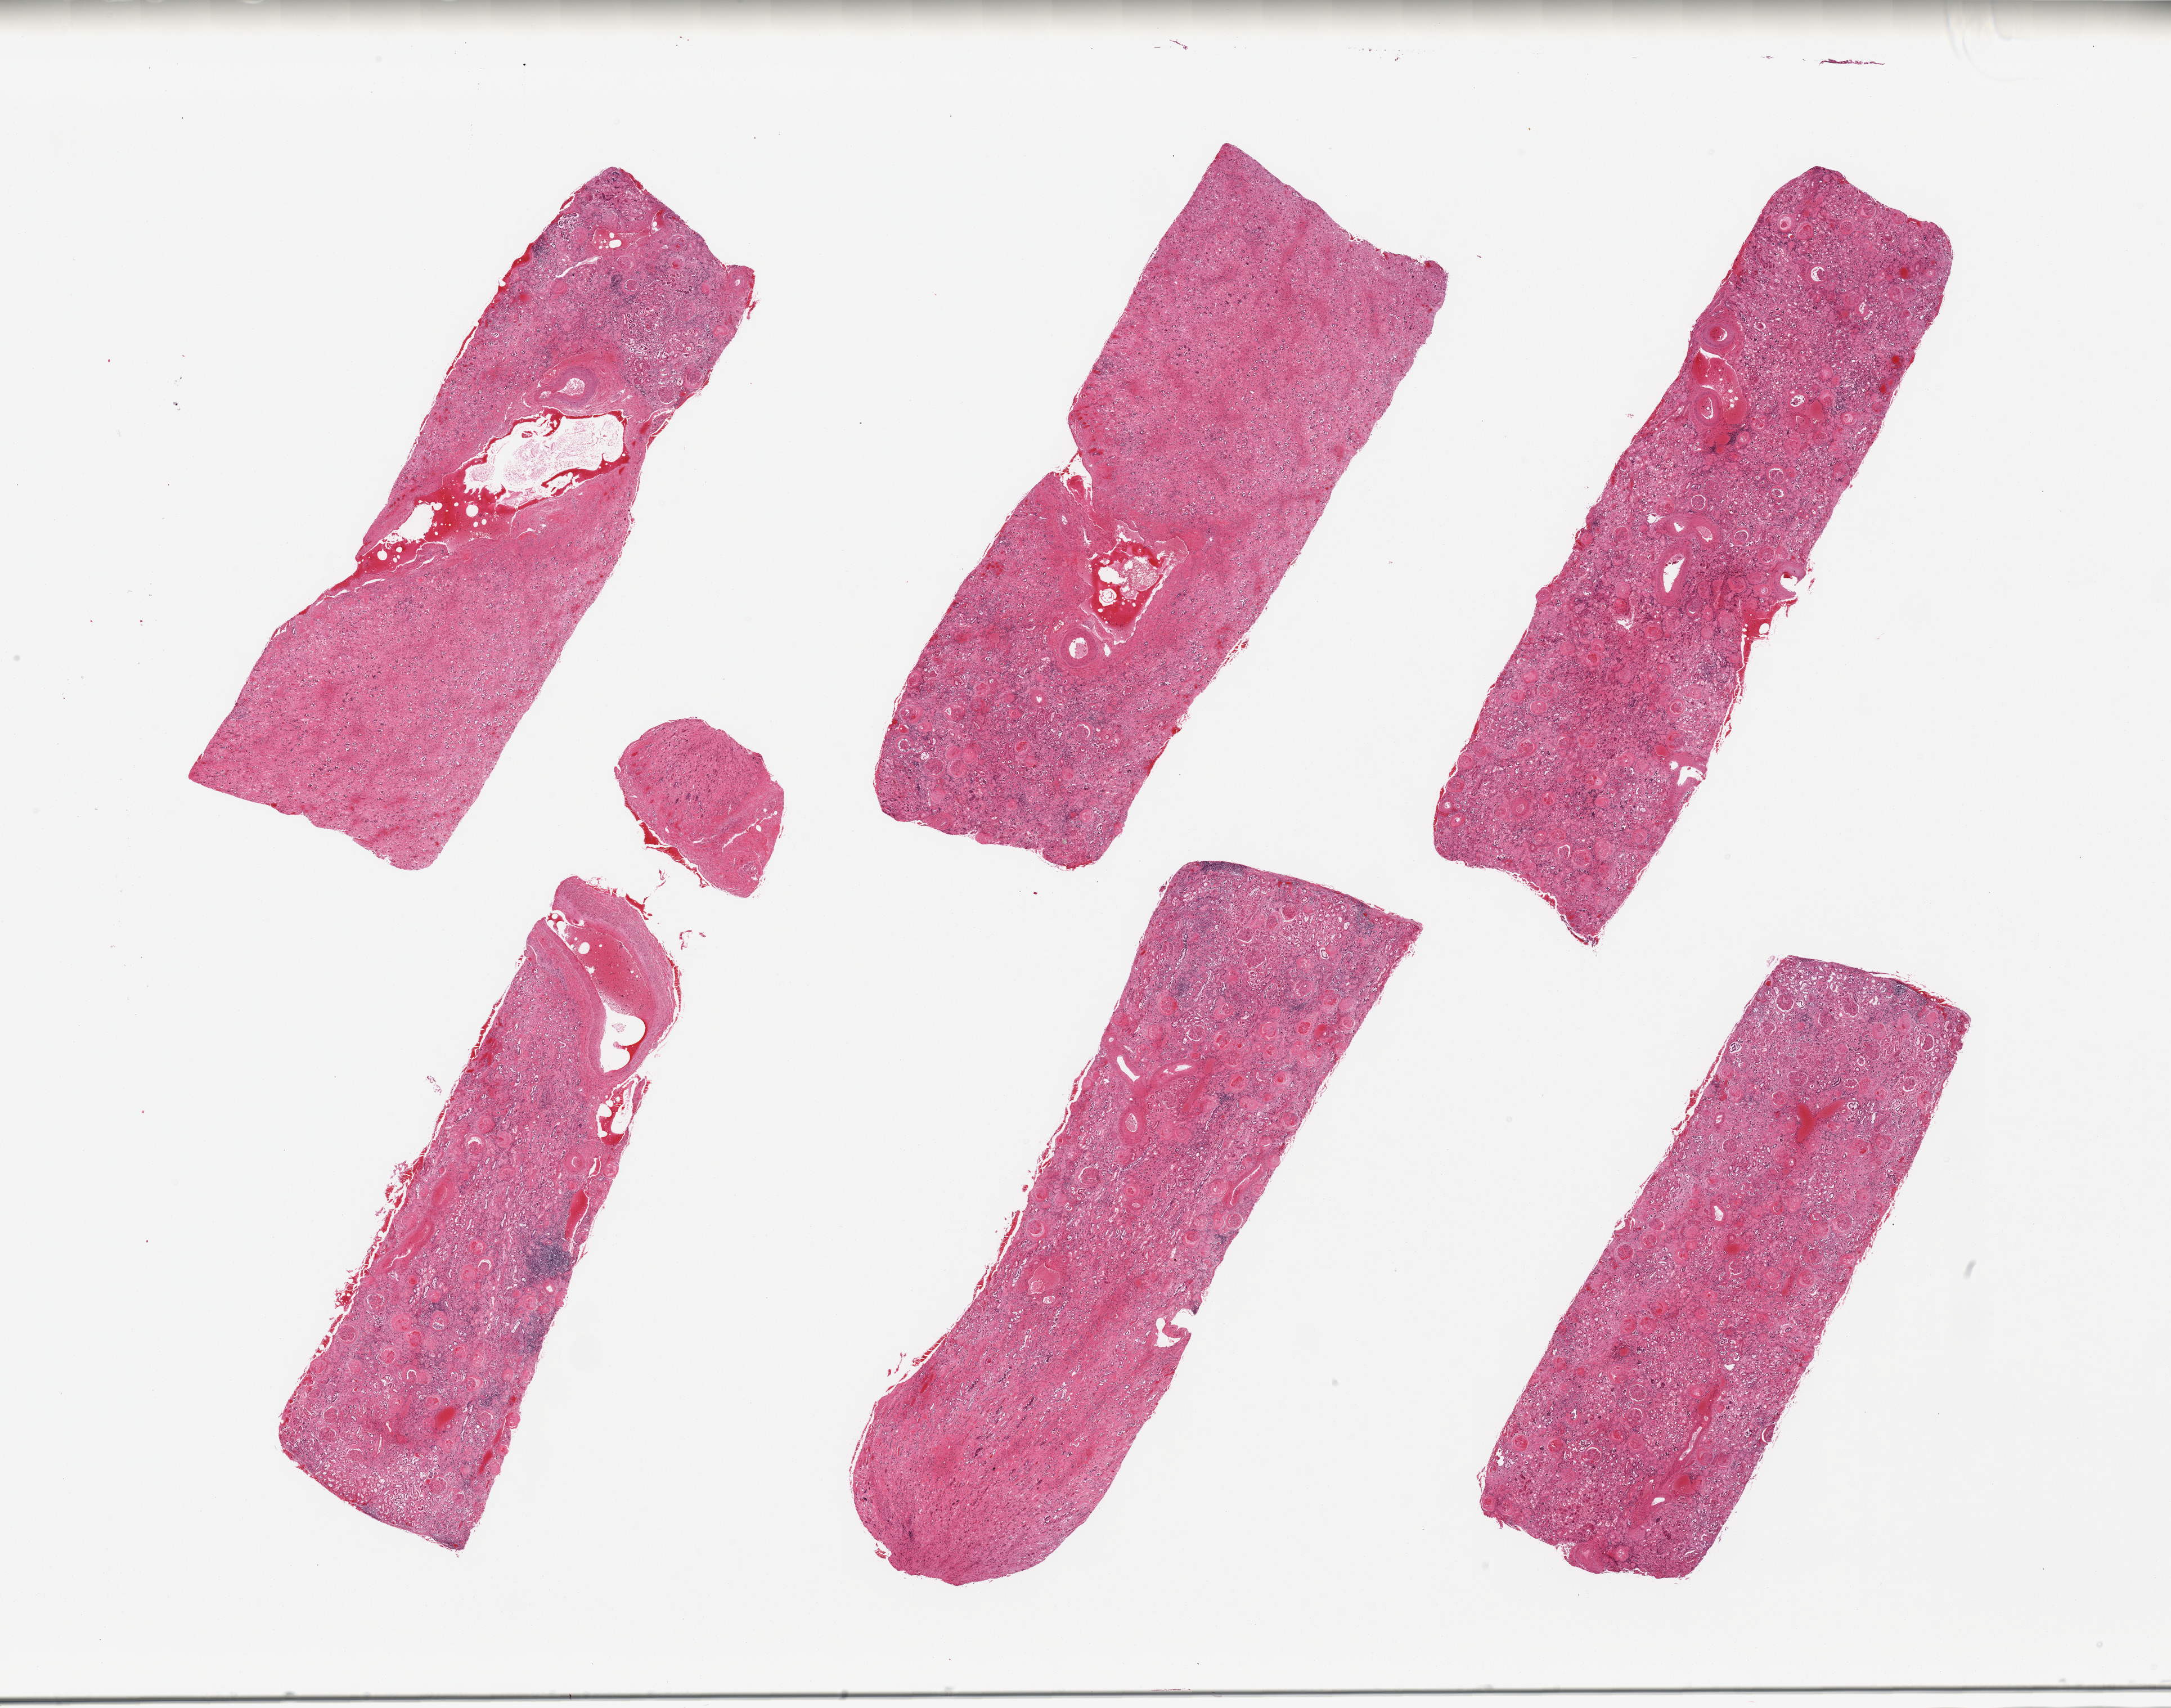
Digitized haematoxylin and eosin-stained section — shown as a low-resolution overview of the whole scanned area (about 30.5 x 24.0 mm, acquisition: 20x scan); PAXgene-fixed paraffin-embedded (PFPE) section; target tissue: renal cortex; tissue donor sample. Donor: male.
* reviewer comment on this tissue sample: 6 pieces; mild to moderate autolysis; arterio- and arteriolo-nephrosclerosis; diabetic nephropathy; nephritis; end stage renal disease